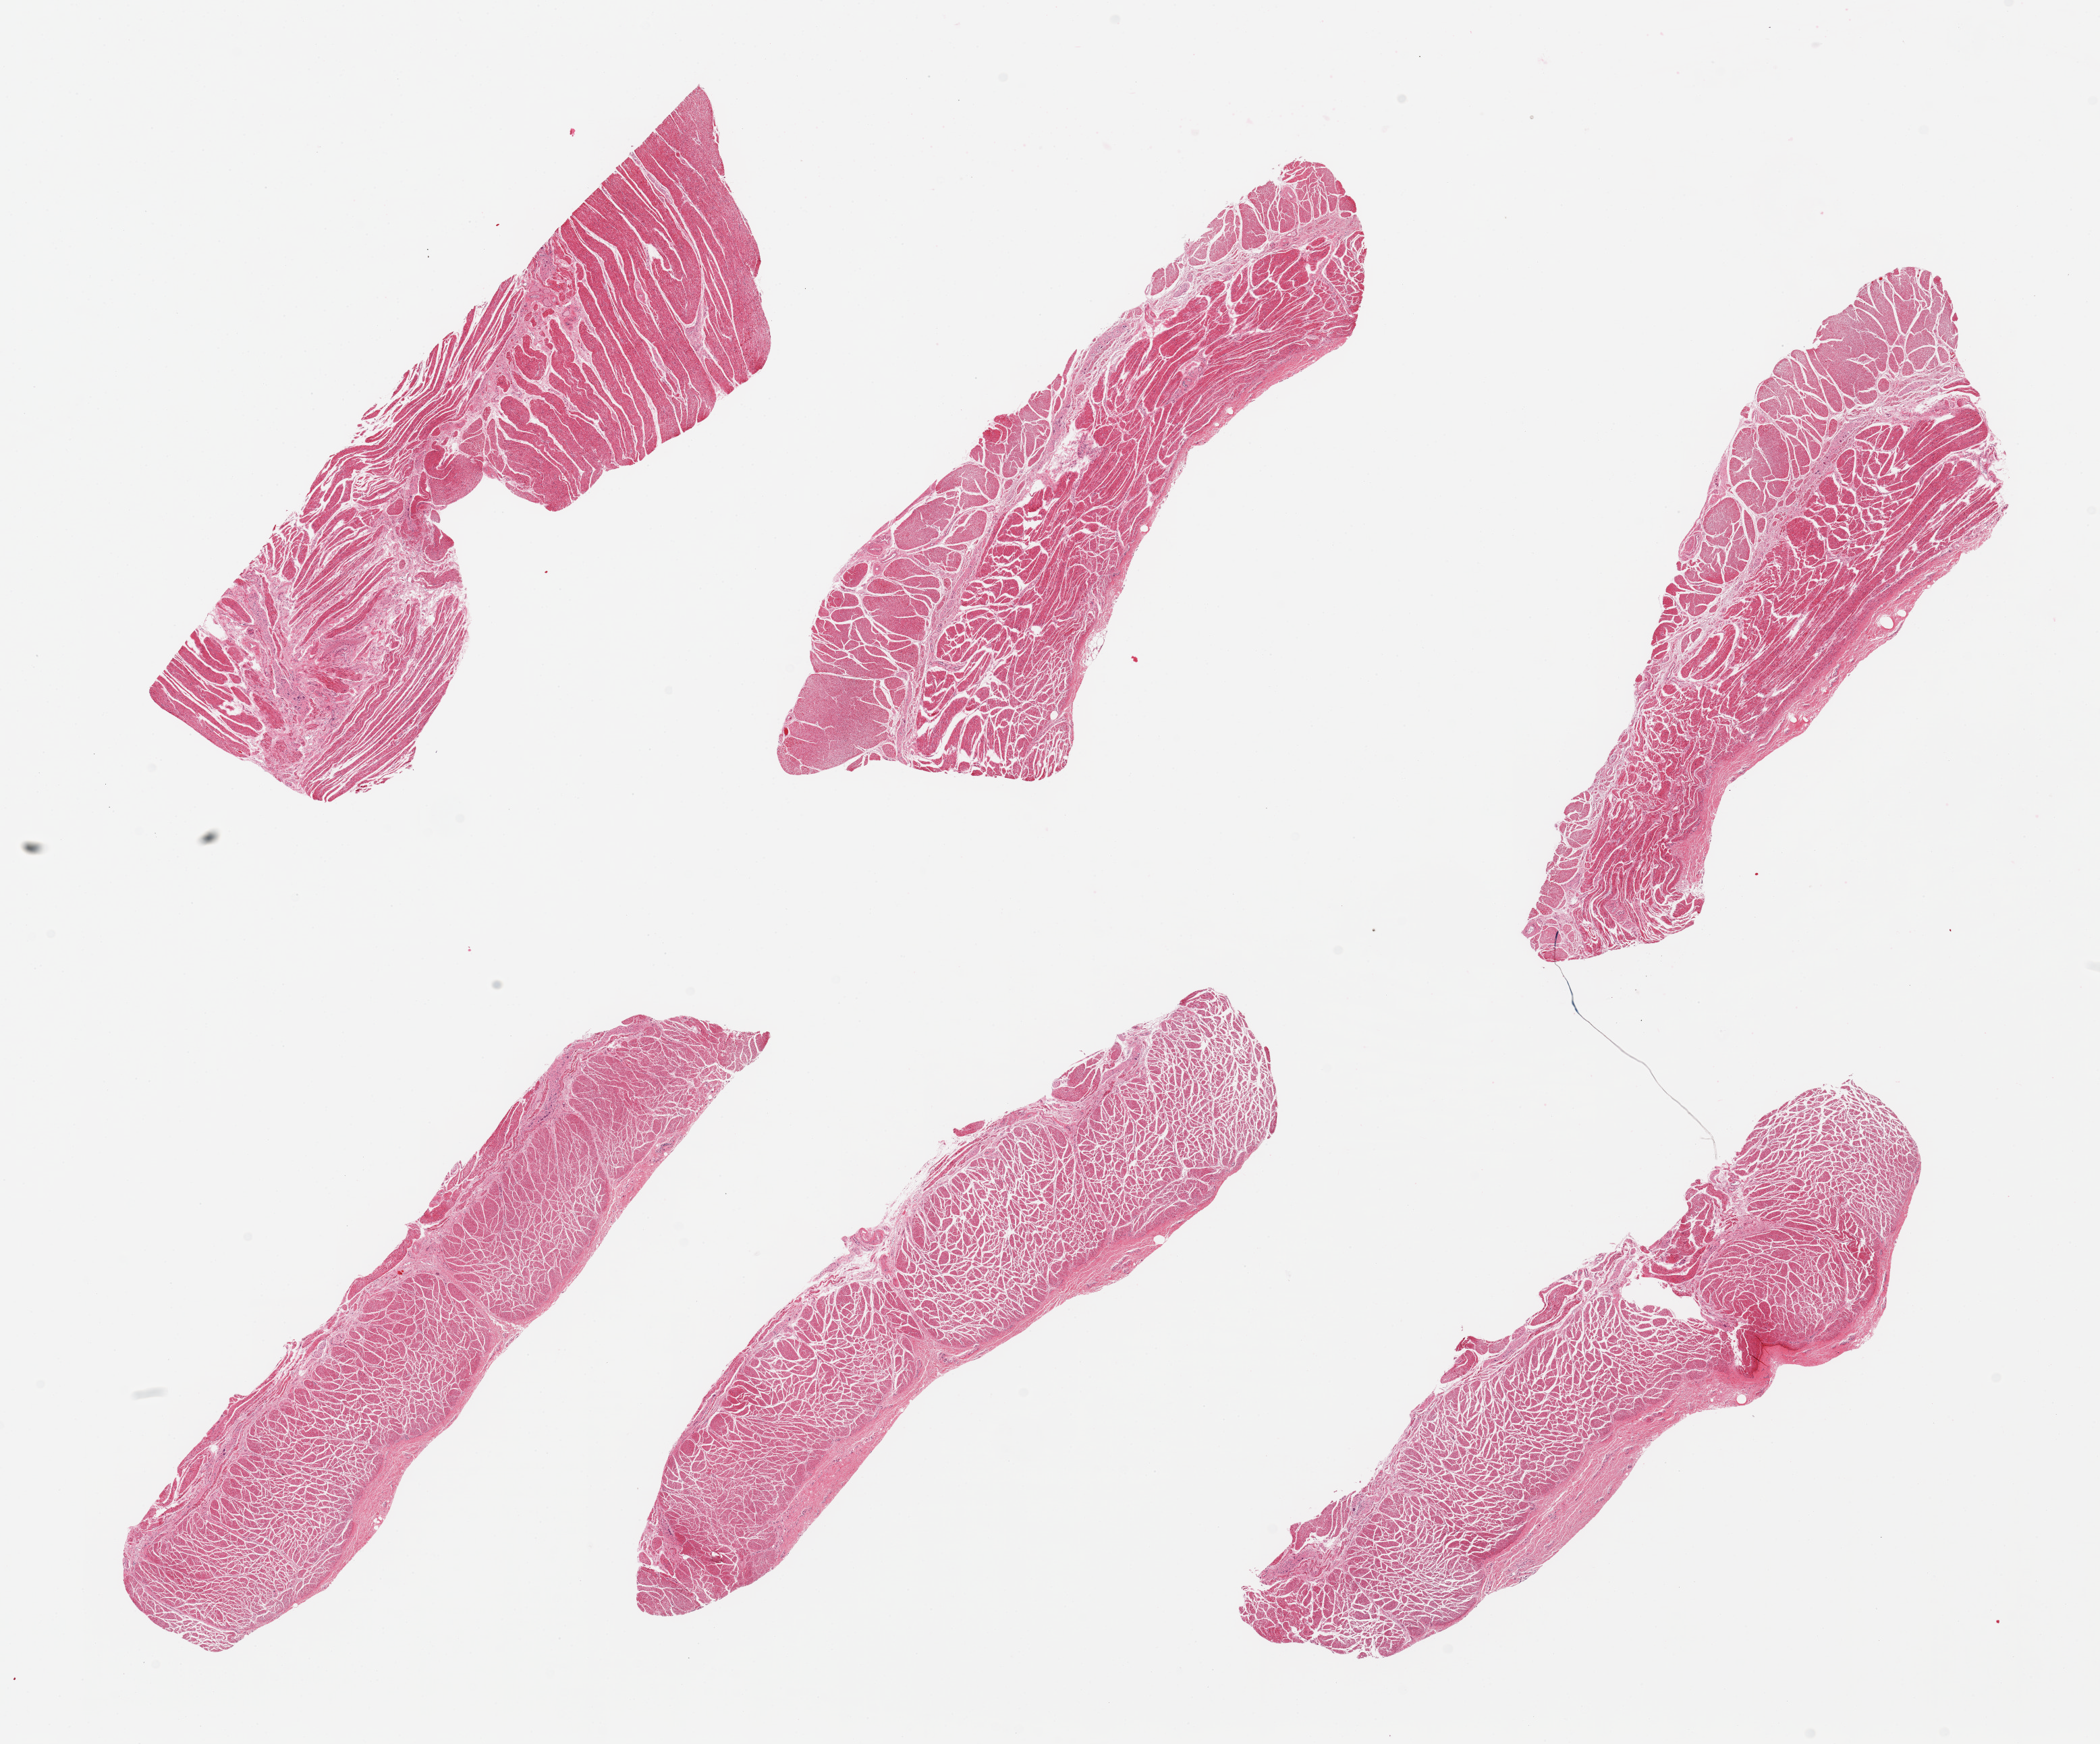
Digitized haematoxylin and eosin-stained section, brightfield — a low-resolution overview of the entire scanned area, about 24.6 x 20.4 mm, PAXgene-fixed, paraffin-embedded tissue, section of gastroesophageal junction (target tissue), tissue donor sample. Male donor.
• pathologist's review note for this sample: 6 pieces; well trimmed